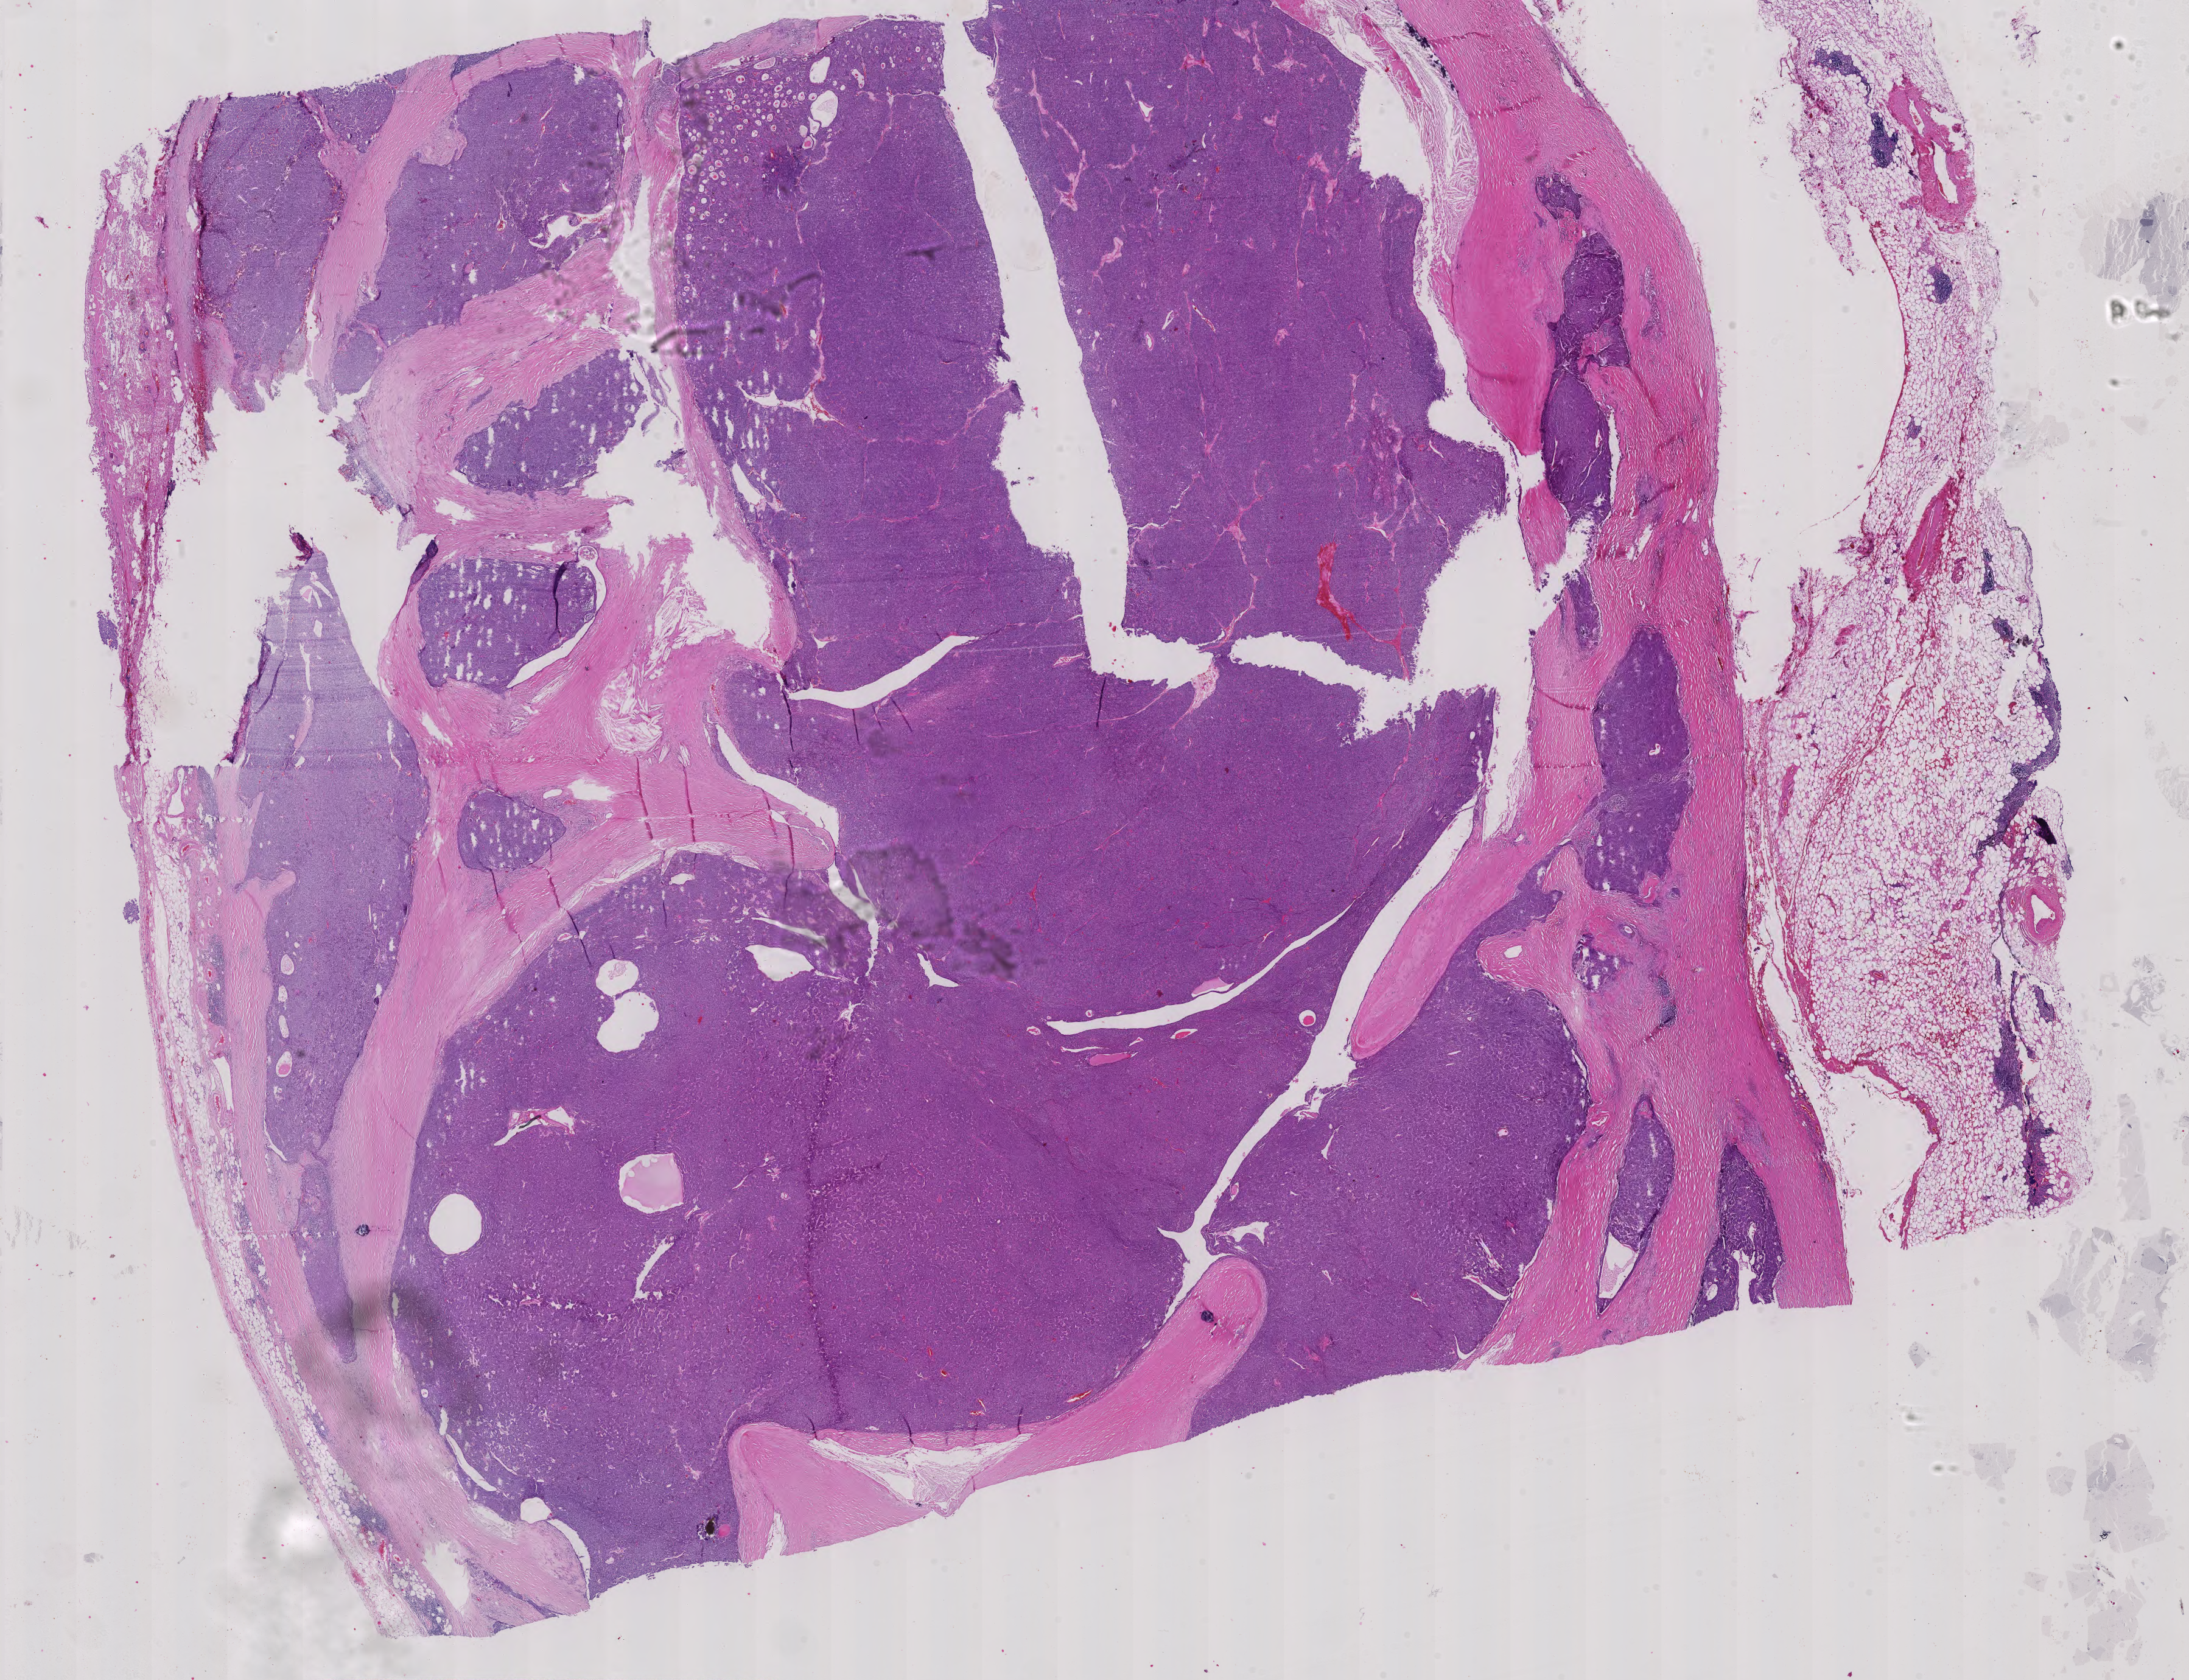
Digitized H&E-stained tissue section (whole slide) — whole scanned area (about 26.2 x 20.1 mm, from a 40x scan) shown as a low-resolution overview, formalin-fixed paraffin-embedded (FFPE) diagnostic section, thymus, primary tumour sample. Male patient; age at initial diagnosis 60 years.
Histologic diagnosis: Thymoma, type A, malignant.